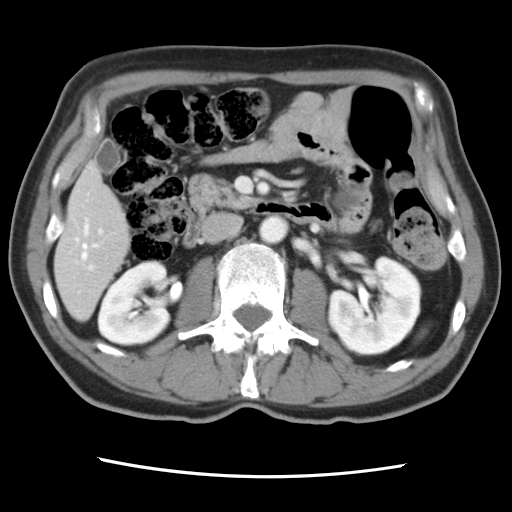
Contrast-enhanced abdominal CT, one axial slice; position 31 of 83 along the scan axis; 120 kVp; intravenous contrast given; soft-tissue window (W 400 / L 40 HU); 5 mm slice thickness; 512 × 512 image matrix, field of view 321 × 321 mm. Male patient, age 69 years. Case-level facts recorded for this patient, not image findings: diagnosis: colorectal cancer liver metastases, imaged before liver resection.
Annotated regions visible in this slice (expert manual segmentation):
- hepatic veins: bounding box [x1, y1, x2, y2] px = [76, 224, 97, 260]
- liver: [55, 166, 130, 319]
- planned liver remnant (the part of the liver to remain after resection): [55, 165, 131, 319]
- portal vein (with intrahepatic branches): [79, 229, 103, 292]